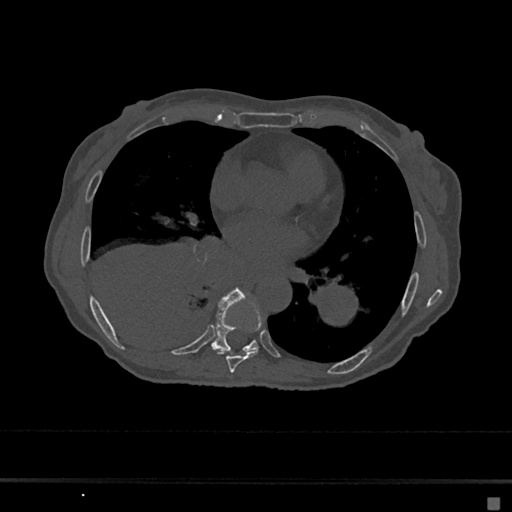
CT including the spine, one axial slice; position 349 of 797 along the scan axis; bone window (W 1800 / L 400 HU); 512 × 512 image matrix, field of view 360 × 360 mm. Patient: female, 68 years. Case-level facts recorded for this patient, not image findings: primary cancer: renal.
Structures marked on this image (semi-automatic segmentation, software-assisted and operator-edited):
- T7 vertebra: bounding box [x1, y1, x2, y2] px = [216, 302, 262, 373]
- T8 vertebra: [211, 288, 258, 354]